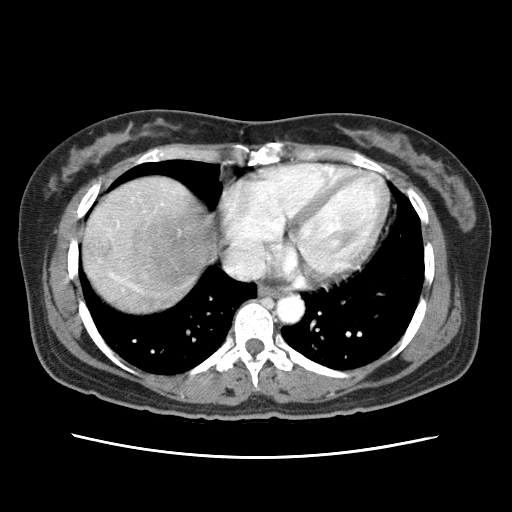
Contrast-enhanced abdominal CT (liver protocol), one axial slice; 120 kVp; soft-tissue window (W 400 / L 40 HU); 2.5 mm slice thickness; 512 × 512 image matrix, field of view 340 × 340 mm. From the clinical record (not read from this slice): diagnosis: hepatocellular carcinoma (patient treated with transarterial chemoembolisation; whether this scan precedes or follows treatment is not stated here); TNM stage (as recorded): Stage-I; Child-Pugh class: A; tumour differentiation: moderately differentiated; tumour nodularity: uninodular.
Structures marked on this image (semi-automatically segmented with operator editing):
- abdominal aorta: bounding box [x1, y1, x2, y2] px = [276, 295, 304, 323]
- liver parenchyma outside the tumour (the mass and vessels are separate outlines, so this box may not span the whole liver): [82, 176, 201, 311]
- mass: [136, 216, 217, 284]
- liver vessels: [110, 224, 119, 279]